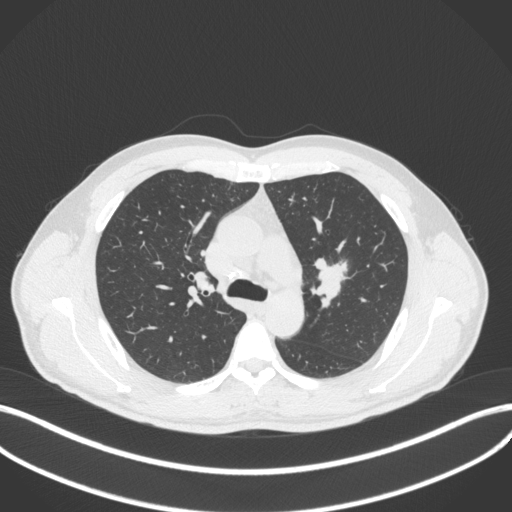
Chest CT, one axial slice. Lung window (W 1500 / L -600 HU). 512 × 512 image matrix. Patient: male, 50 years. From the clinical record (not read from this slice): clinical TNM (as recorded): T1c N1 M1b.
Annotated regions visible in this slice (rectangle marked by the reading radiologist):
- lung tumour (recorded histology: squamous cell carcinoma): bounding box <310,257,352,311> (left, top, right, bottom; pixels)